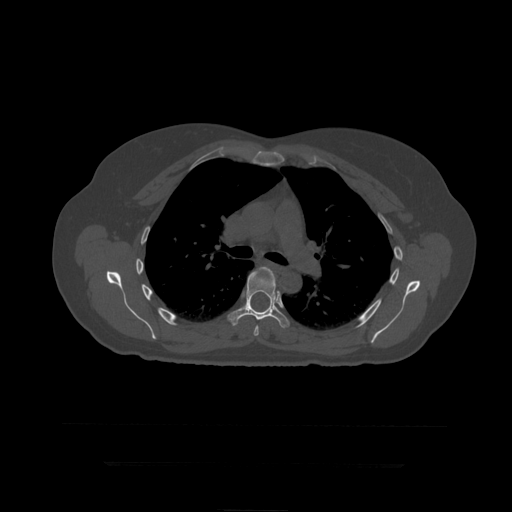
CT including the spine, one axial slice; slice 306 of 399 in the series (ordered by position); reconstruction kernel STANDARD; bone window (W 1800 / L 400 HU); 1.25 mm slice thickness; 512 × 512 image matrix, field of view 450 × 450 mm. Patient age 41 years. From the clinical record (not read from this slice): primary cancer: breast.
Outlined on this slice (semi-automatic segmentation, software-assisted and operator-edited):
- T6 vertebra: bounding box (x1, y1, x2, y2) in pixels: (254, 267, 275, 336)
- T7 vertebra: (228, 267, 290, 329)